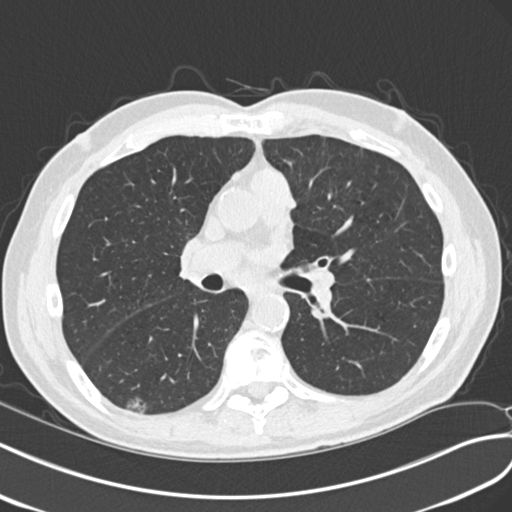
Low-dose screening chest CT, axial slice, second screening round (one year after baseline), lung window (W 1500 / L -600 HU), standard (soft-tissue) reconstruction kernel (B30f), 512 × 512 image matrix. Male participant, aged 68 years at enrolment.
• Expert reader's lesion annotation, box from (x=110, y=384) to (x=160, y=421) px.
• The screening reader recorded 4 non-calcified nodules or masses ≥4 mm on this exam (right upper lobe, left upper lobe, right upper lobe, right lower lobe); which of them this box marks is not recorded.